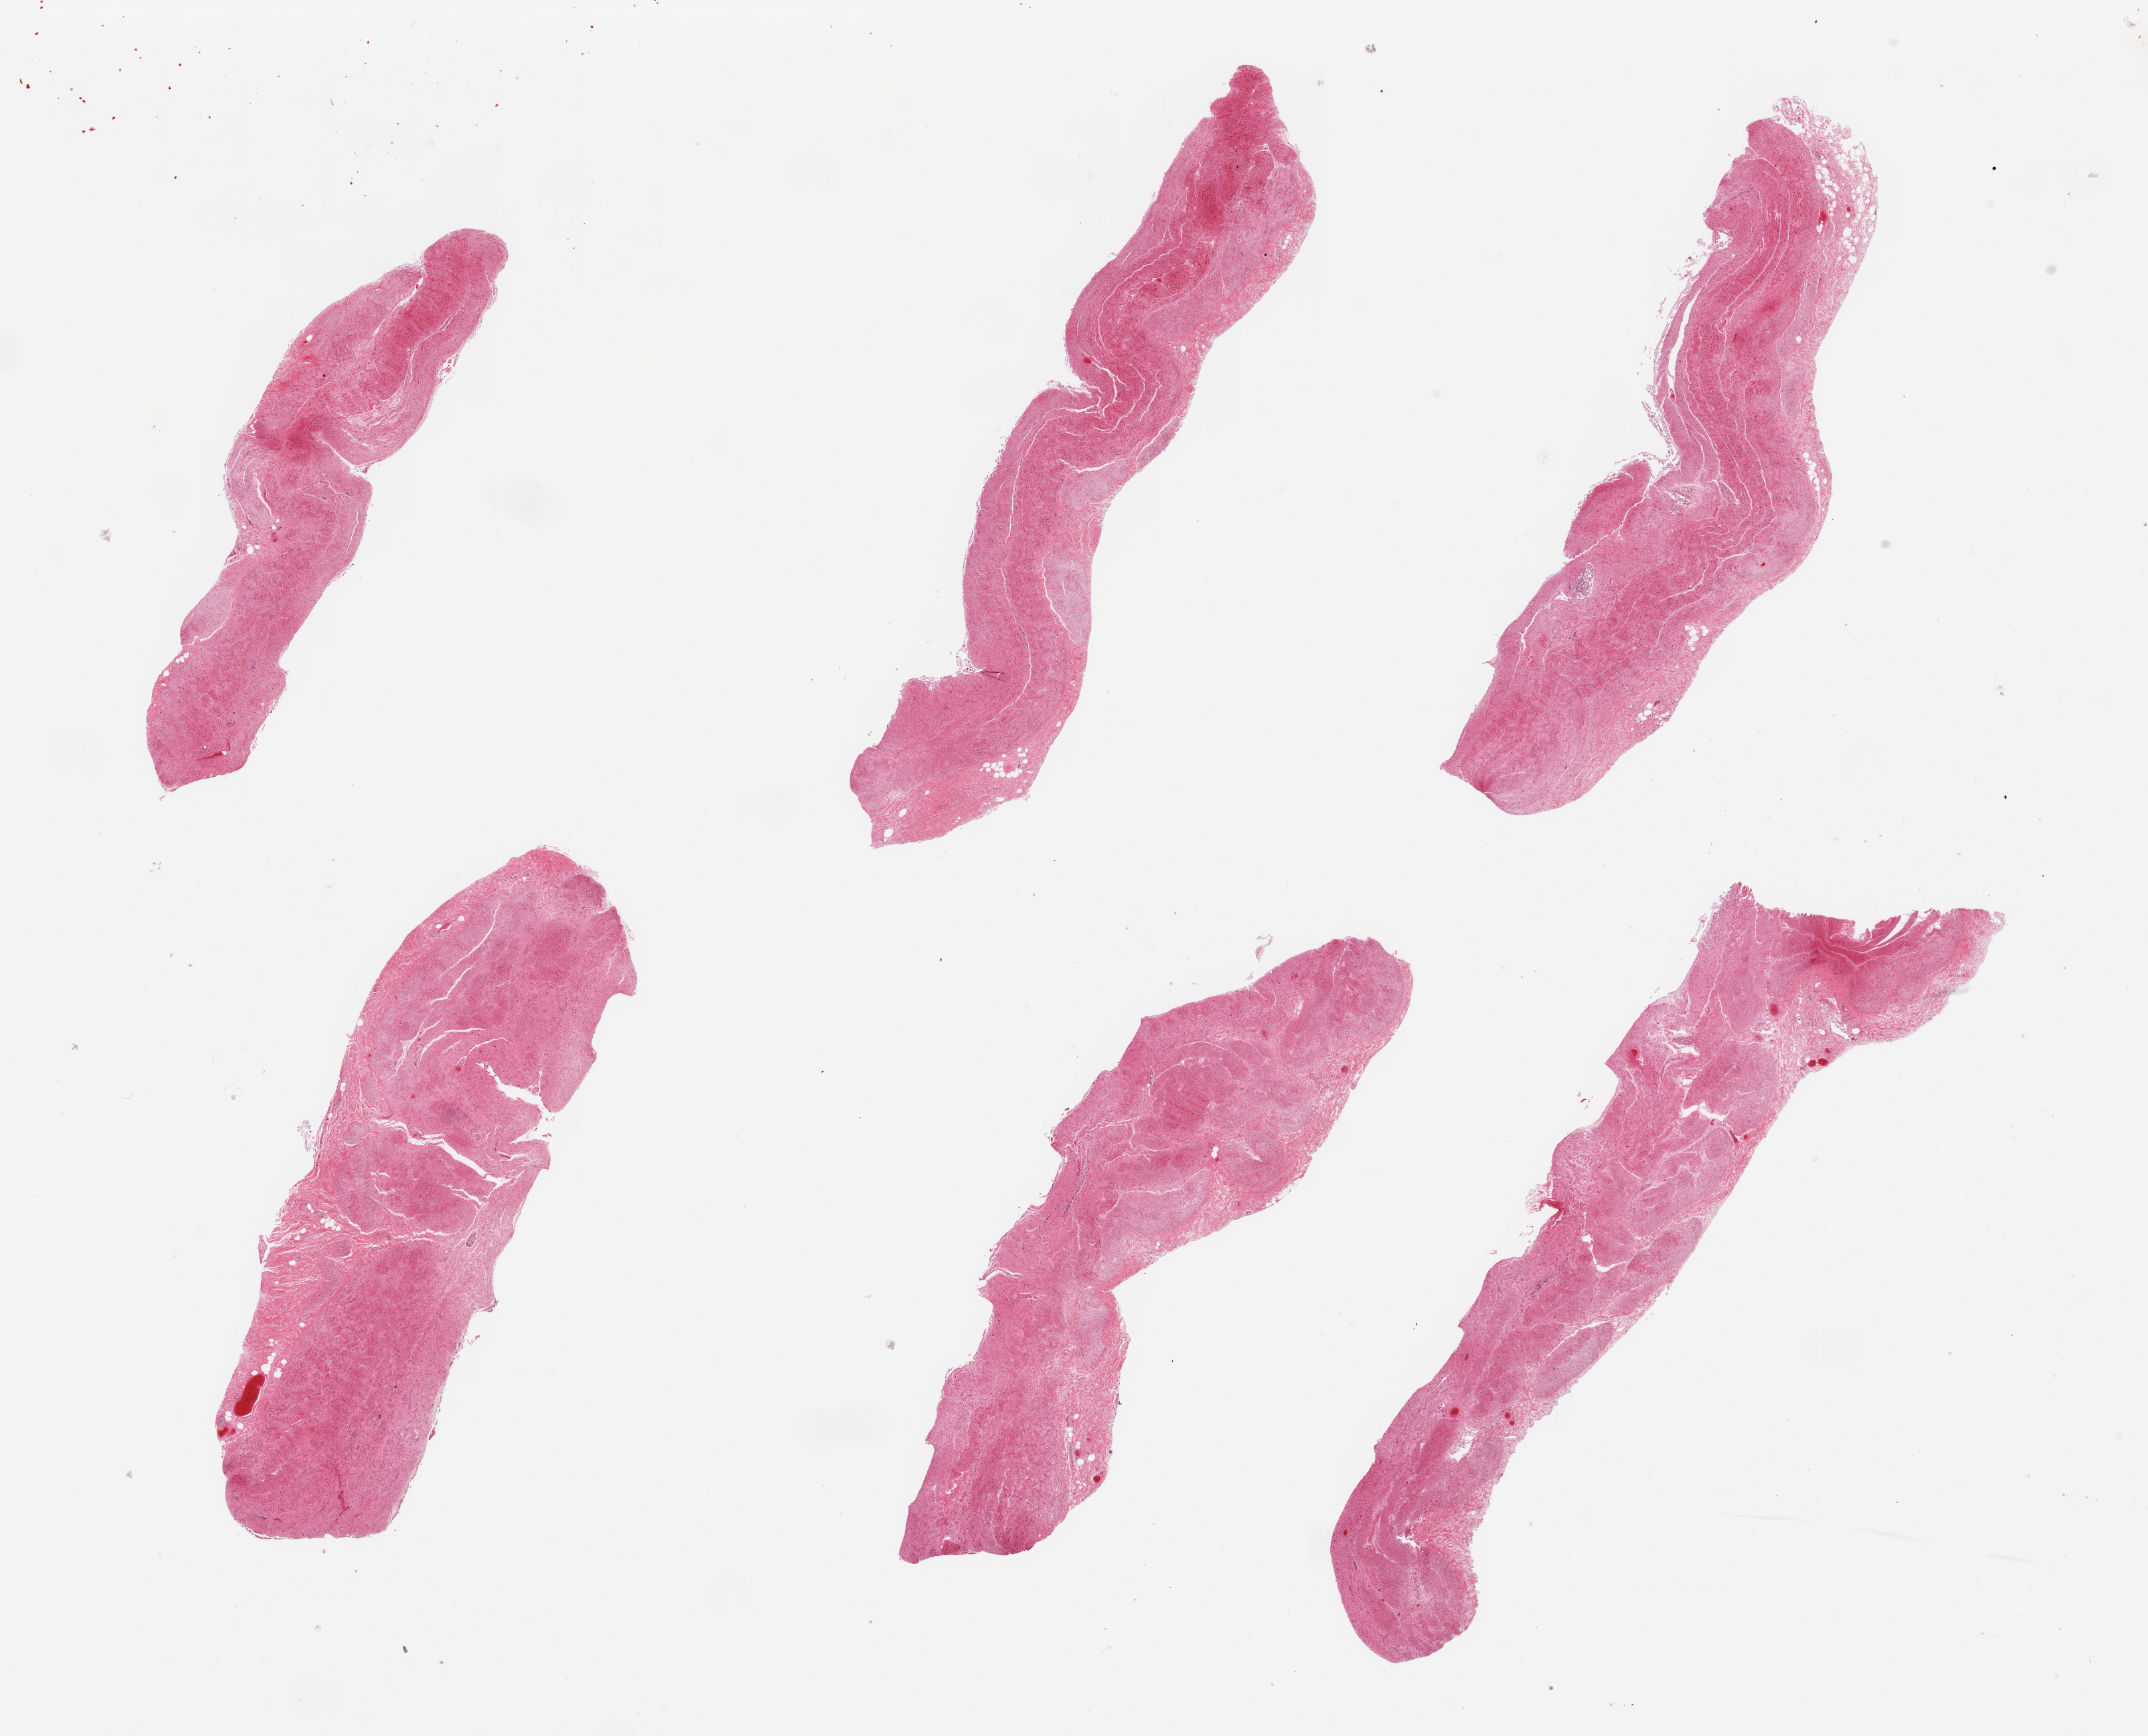
Digitized hematoxylin and eosin (H&E)-stained section, brightfield — low-resolution overview of the scanned area, about 25.6 x 20.7 mm, PAXgene-fixed, paraffin-embedded tissue, sampled site (target tissue): stomach, donor tissue sample. Donor: male.
Pathologist's review note for this sample: 6 pieces, viable muscularis only, mucosa completely sloughed.